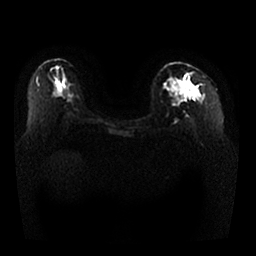
Breast MRI, one axial slice; position 17 of 25 along the scan axis; diffusion-weighted series; image 2 of 4 stored at this slice position (different b-values; order by instance number); 1.5 T; 4 mm slice thickness; 256 × 256 image matrix, field of view 350 × 350 mm. Female patient.
Annotated regions visible in this slice (expert manual segmentation):
- tumour on diffusion-weighted imaging: bounding box [x1, y1, x2, y2] px = [179, 86, 195, 97]